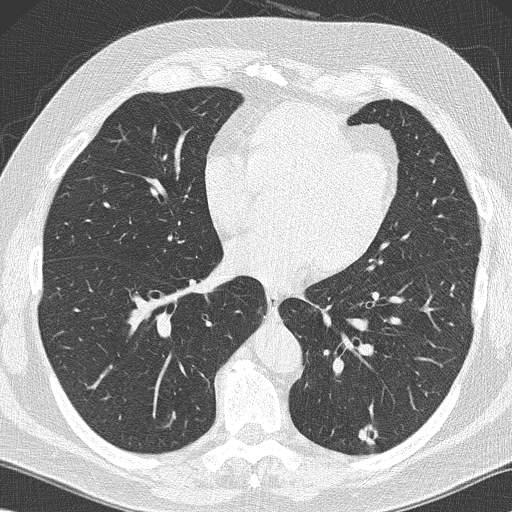
Axial slice from a low-dose chest CT screening exam; baseline annual screen; lung window (W 1500 / L -600 HU); lung (sharp) reconstruction kernel (B50f). Male, age 59 years at enrolment. Former smoker at enrolment.
Expert-annotated lung lesion, box from (x=345, y=416) to (x=387, y=453) px. The screening reader recorded 2 non-calcified nodules or masses ≥4 mm on this exam; which of them this box marks is not recorded. Later outcome: lung cancer diagnosed 61 days after this screen — large cell carcinoma, NOS, left lower lobe, poorly differentiated (G3), stage IA (AJCC 6th edition), 14 mm at pathology.